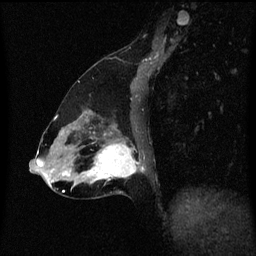
Breast MRI (dynamic contrast-enhanced), one sagittal slice; slice 26 of 60 in the series (ordered by position); dynamic contrast-enhanced series, image 2 of 3 at this slice position (ordered by acquisition); 1.5 T; TE 4.2 ms, TR 8.4 ms; 2 mm slice thickness; 256 × 256 image matrix. Female patient, age 47 years.
Structures marked on this image (semi-automatic segmentation, software-assisted and operator-edited):
- analysis volume of interest (the breast-tissue region the enhancement analysis was run in; not a lesion): bounding box [x1, y1, x2, y2] px = [85, 136, 143, 195]
- tumour enhancement mask (voxels above the 70 % enhancement threshold inside the analysis volume of interest): [85, 142, 141, 181]